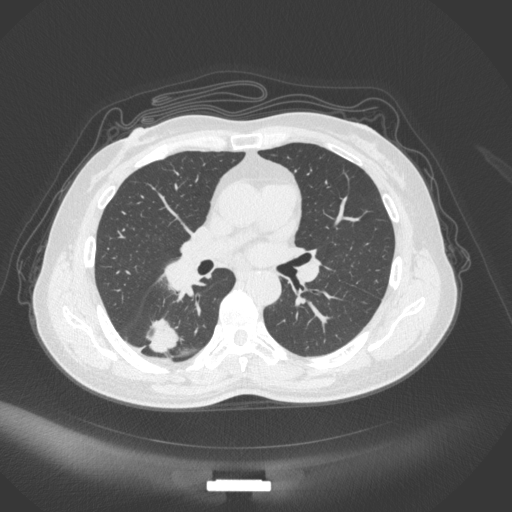
Chest CT, one axial slice. Position 167 of 352 along the scan axis. Reconstruction kernel B31f. 120 kVp. Lung window (W 1500 / L -600 HU). 1 mm slice thickness. 512 × 512 image matrix, field of view 400 × 400 mm. Female patient, age 55 years. Case-level facts recorded for this patient, not image findings: clinical TNM (as recorded): T1c N1 M0.
Outlined on this slice (bounding box drawn by a radiologist):
- lung tumour (recorded histology: adenocarcinoma): box from (x=143, y=314) to (x=182, y=353) px